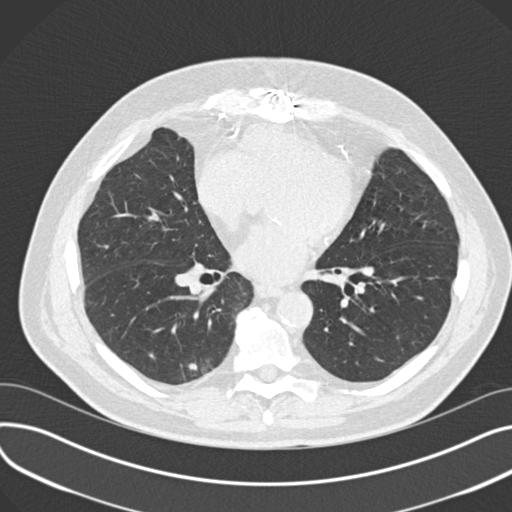
Low-dose screening chest CT, one axial slice. Slice 80 of 177 in the series (ordered by position). 120 kVp. Lung window (W 1500 / L -600 HU). 2 mm slice thickness. 512 × 512 image matrix.
Outlined on this slice (expert manual segmentation):
- lesion 1 (tumor, lower lobe of right lung): bounding box [x1, y1, x2, y2] px = [188, 363, 198, 371]